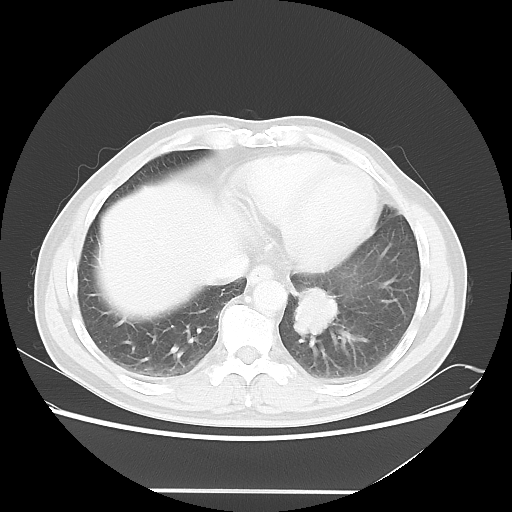
Chest CT, one axial slice; position 15 of 53 along the scan axis; reconstruction kernel LUNG; 120 kVp; lung window (W 1500 / L -600 HU); 5 mm slice thickness; 512 × 512 image matrix, field of view 385 × 385 mm. Patient: male, 61 years. From the clinical record (not read from this slice): clinical TNM (as recorded): T1c N0 M0; histopathological grade: G3.
Outlined on this slice (rectangle marked by the reading radiologist):
- lung tumour (recorded histology: adenocarcinoma): box from (x=288, y=280) to (x=342, y=348) px